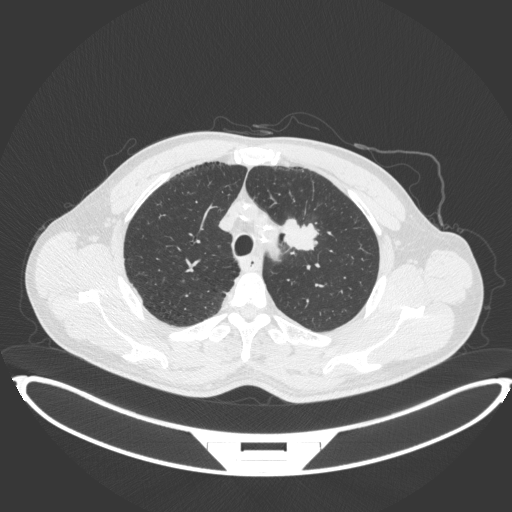
Chest CT, one axial slice. Slice 341 of 407 in the series (ordered by position). Reconstruction kernel B31f. 120 kVp. Lung window (W 1500 / L -600 HU). 512 × 512 image matrix. Patient: male, 60 years. Case-level facts recorded for this patient, not image findings: clinical TNM (as recorded): T2a N0 M0; histopathological grade: G1-G2.
Outlined on this slice (bounding box drawn by a radiologist):
- lung tumour (recorded histology: squamous cell carcinoma): bounding box (x1, y1, x2, y2) in pixels: (277, 215, 320, 253)